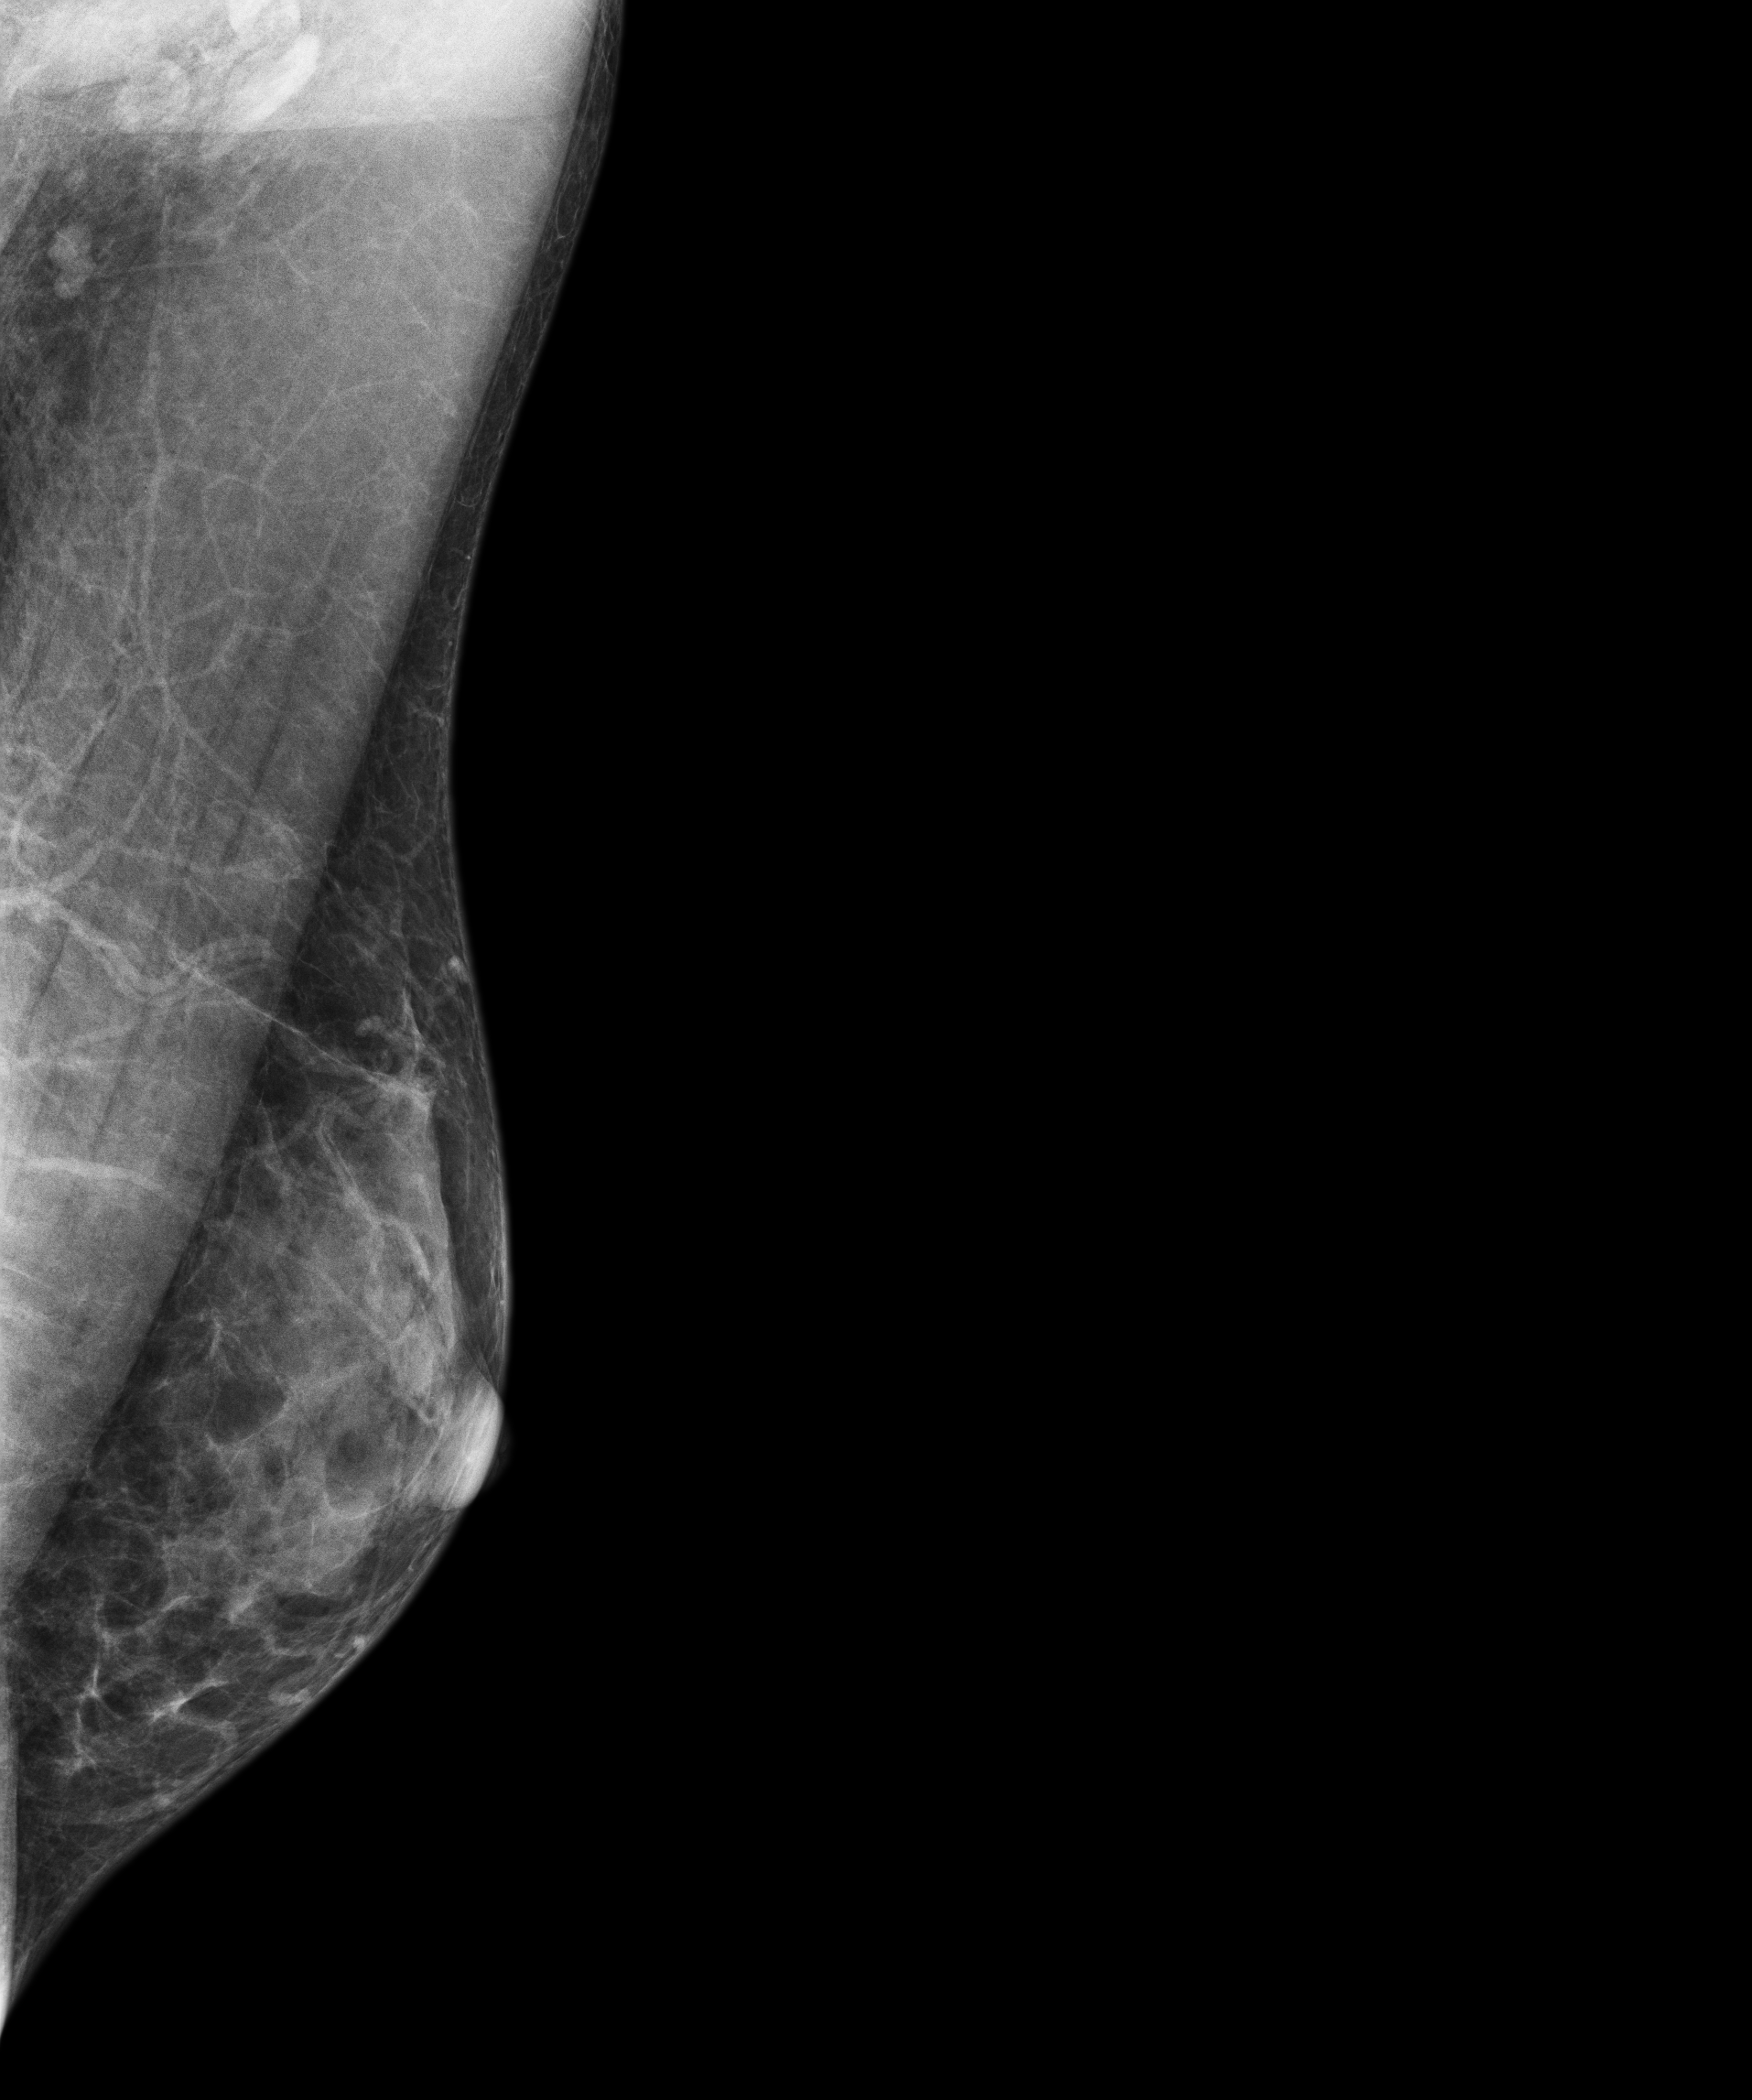
Digital mammogram (FFDM); left breast; MLO view; screening examination; compressed breast thickness 30 mm; system: Senographe Essential ADS_56.21.3. Female patient, age 55 years.
BI-RADS breast density category at the screening exam (both breasts, scale 1–4): 4. Final BI-RADS category for the screening round (tomosynthesis exam, both breasts): category 1. Recall: no recall after this screen.